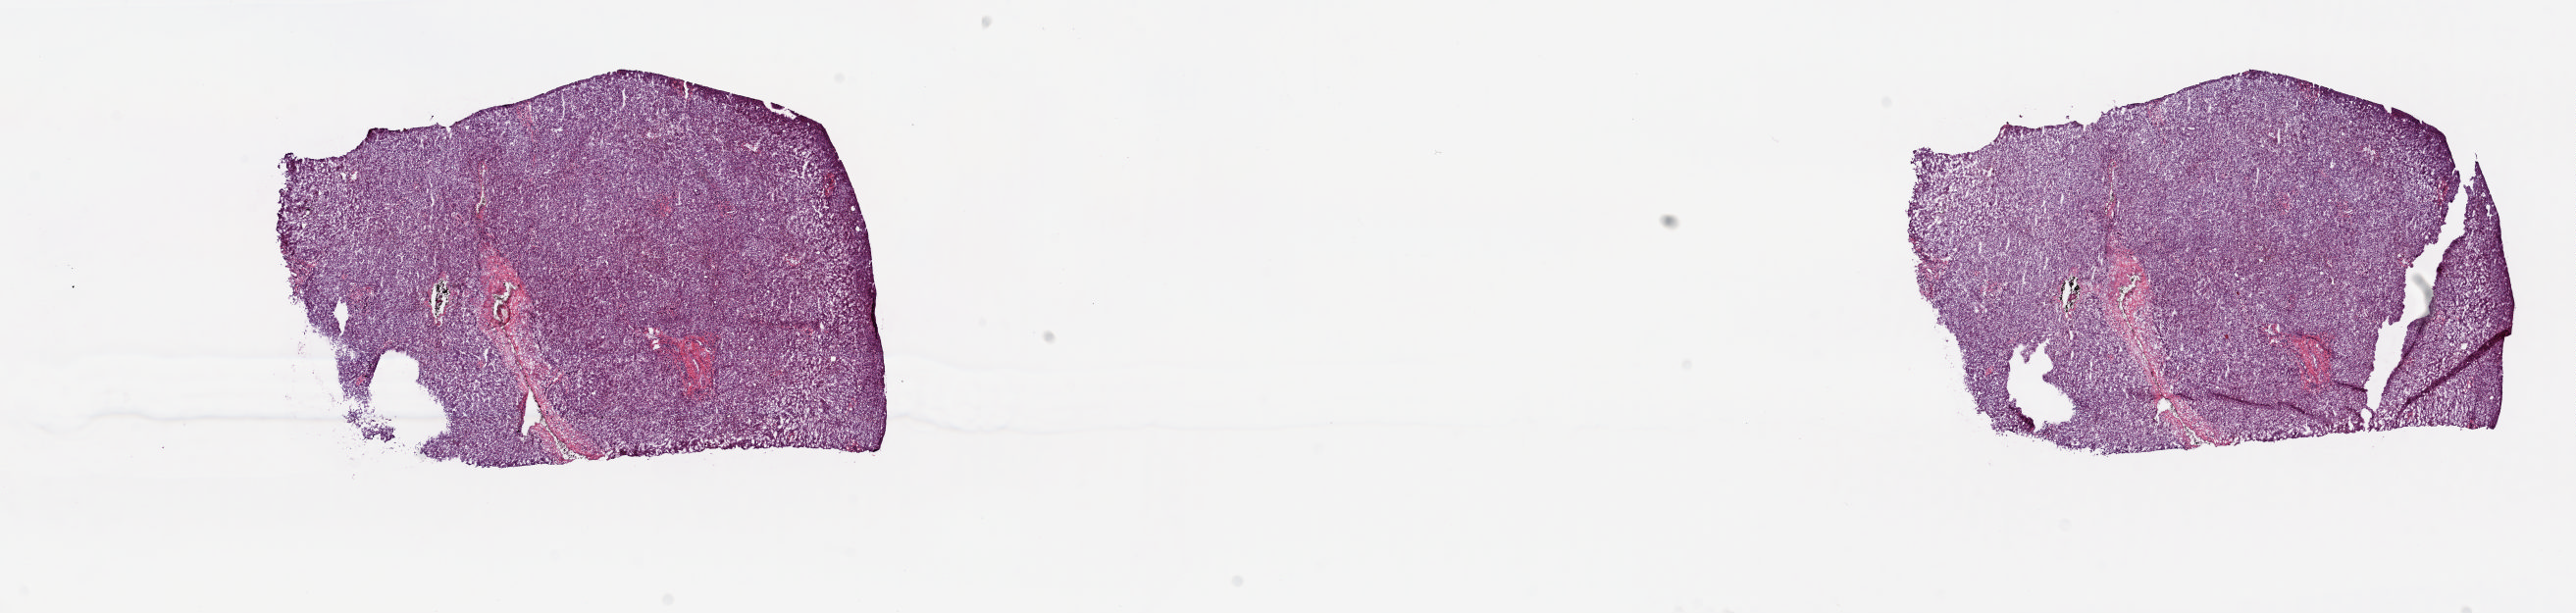
Digitized H&E tissue section (whole slide) — a low-resolution overview of the entire scanned area, about 20.8 x 5.0 mm; frozen section; bile duct, solid tissue normal (non-tumour tissue) sample. Patient: male, age at initial diagnosis 60 years. Slide review estimates, as recorded: tumour cells 0%, tumour nuclei 0%, normal cells 100%, stromal cells 0%, necrosis 0%. Infiltration values recorded for this section: lymphocyte infiltration 2%, monocyte infiltration 0%, neutrophil infiltration 0%.
• this section: solid tissue normal sample (biorepository sample class)
• patient diagnosis: Cholangiocarcinoma (intrahepatic bile duct)